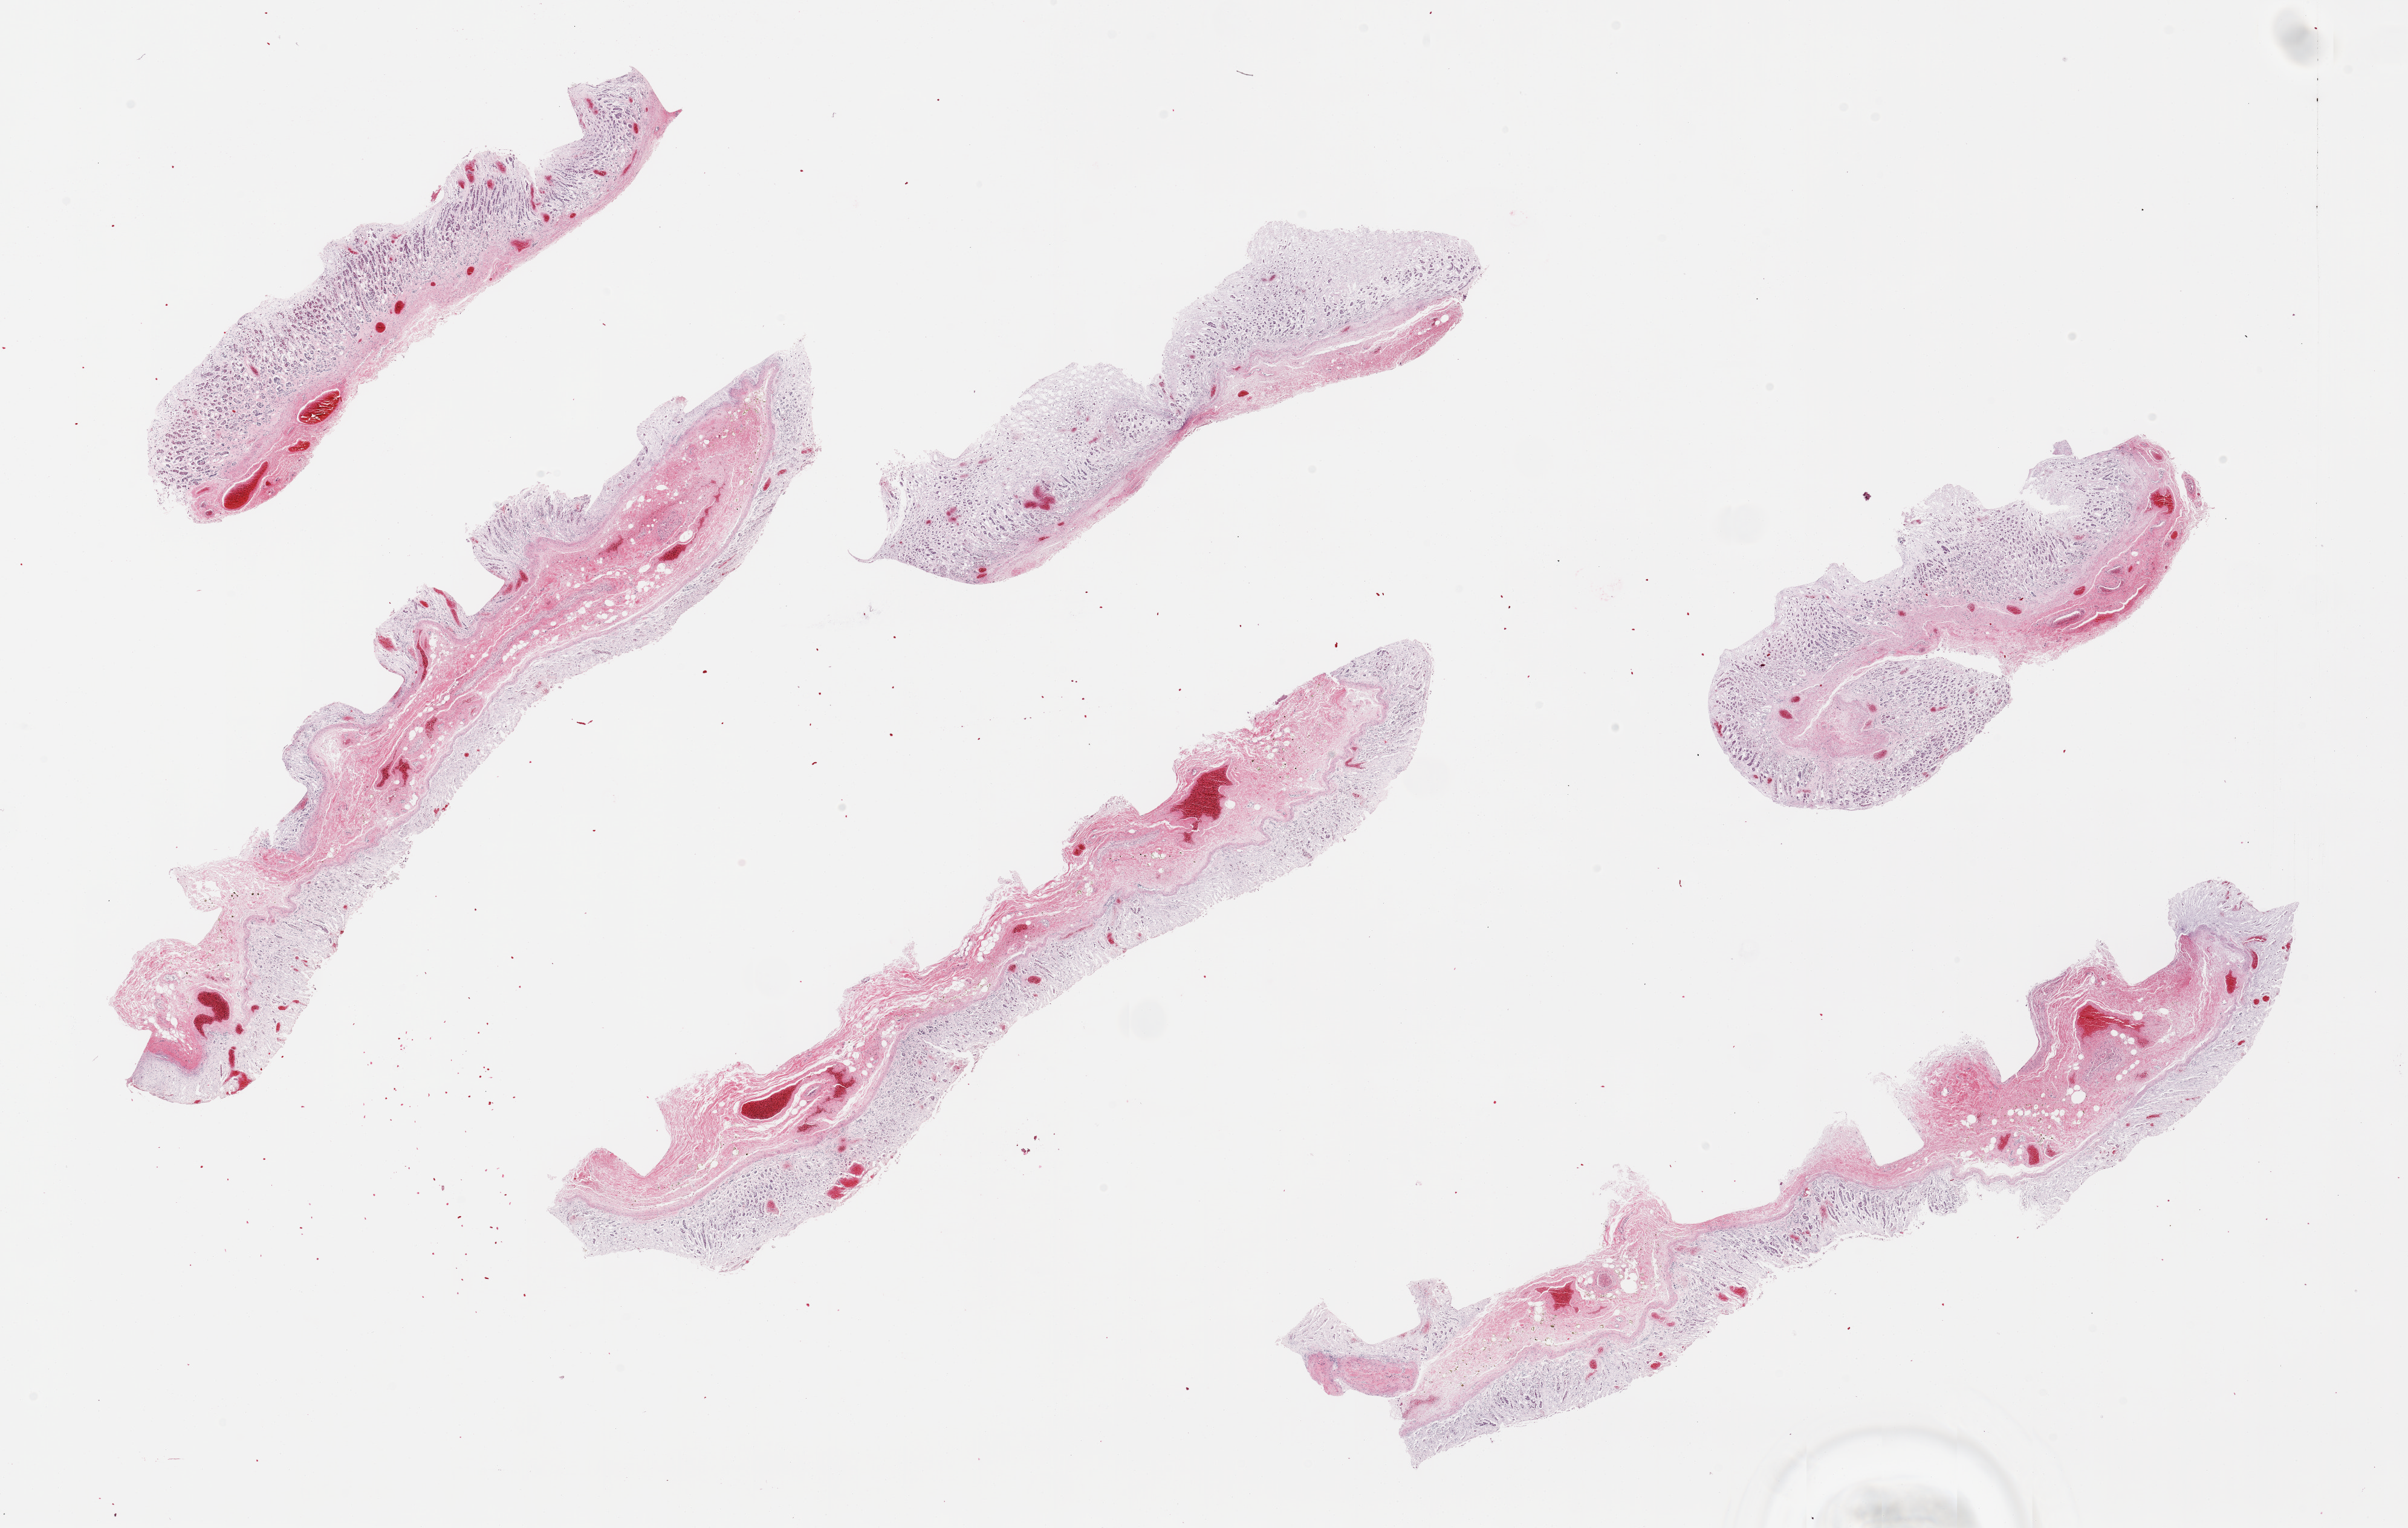
Whole-slide image, H&E stain, shown as a low-resolution overview of the whole scanned area (about 31.5 x 20.0 mm, from a 20x scan); PAXgene-fixed, paraffin-embedded tissue; target tissue: stomach; donor tissue sample. Donor: male.
Reviewer comment on this tissue sample: 6 pieces; too autolyzed.